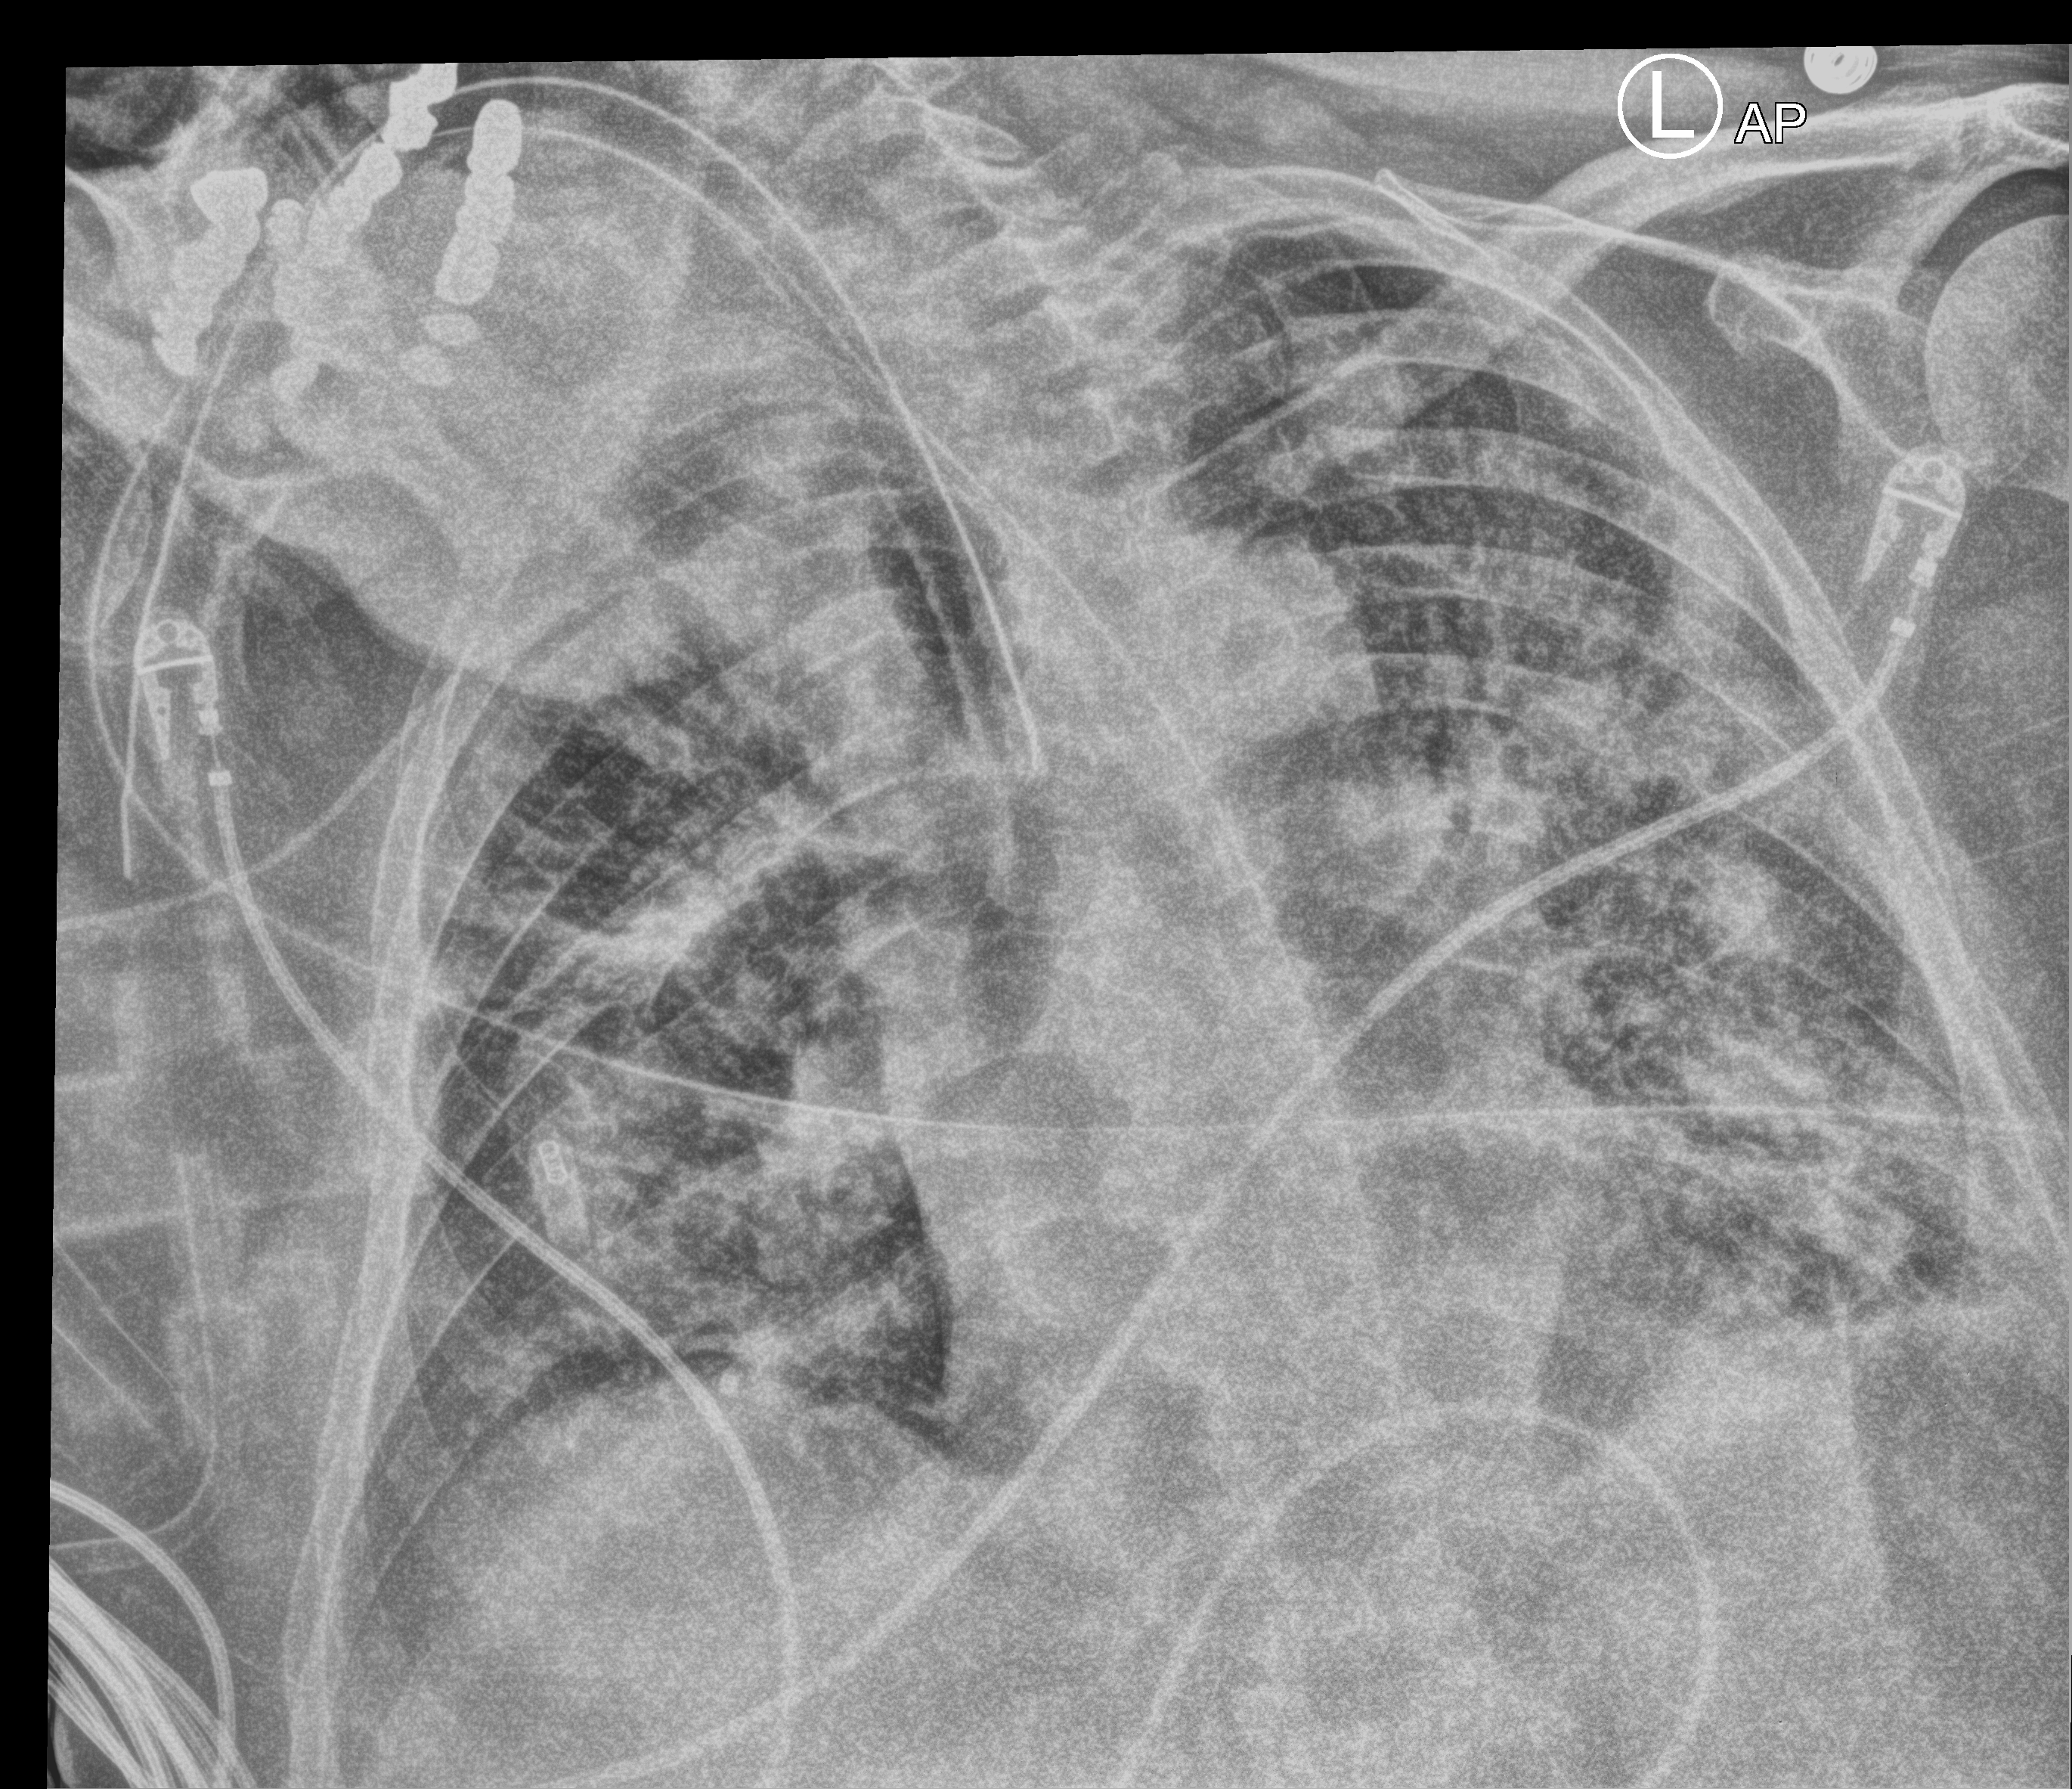
Bedside chest radiograph (computed radiography); anteroposterior (AP) projection. Male patient hospitalised with COVID-19, age 60–74 years.
Hospital-stay facts (about this admission, not read from this image; timing relative to this image not recorded):
- hypertension (admission record): no